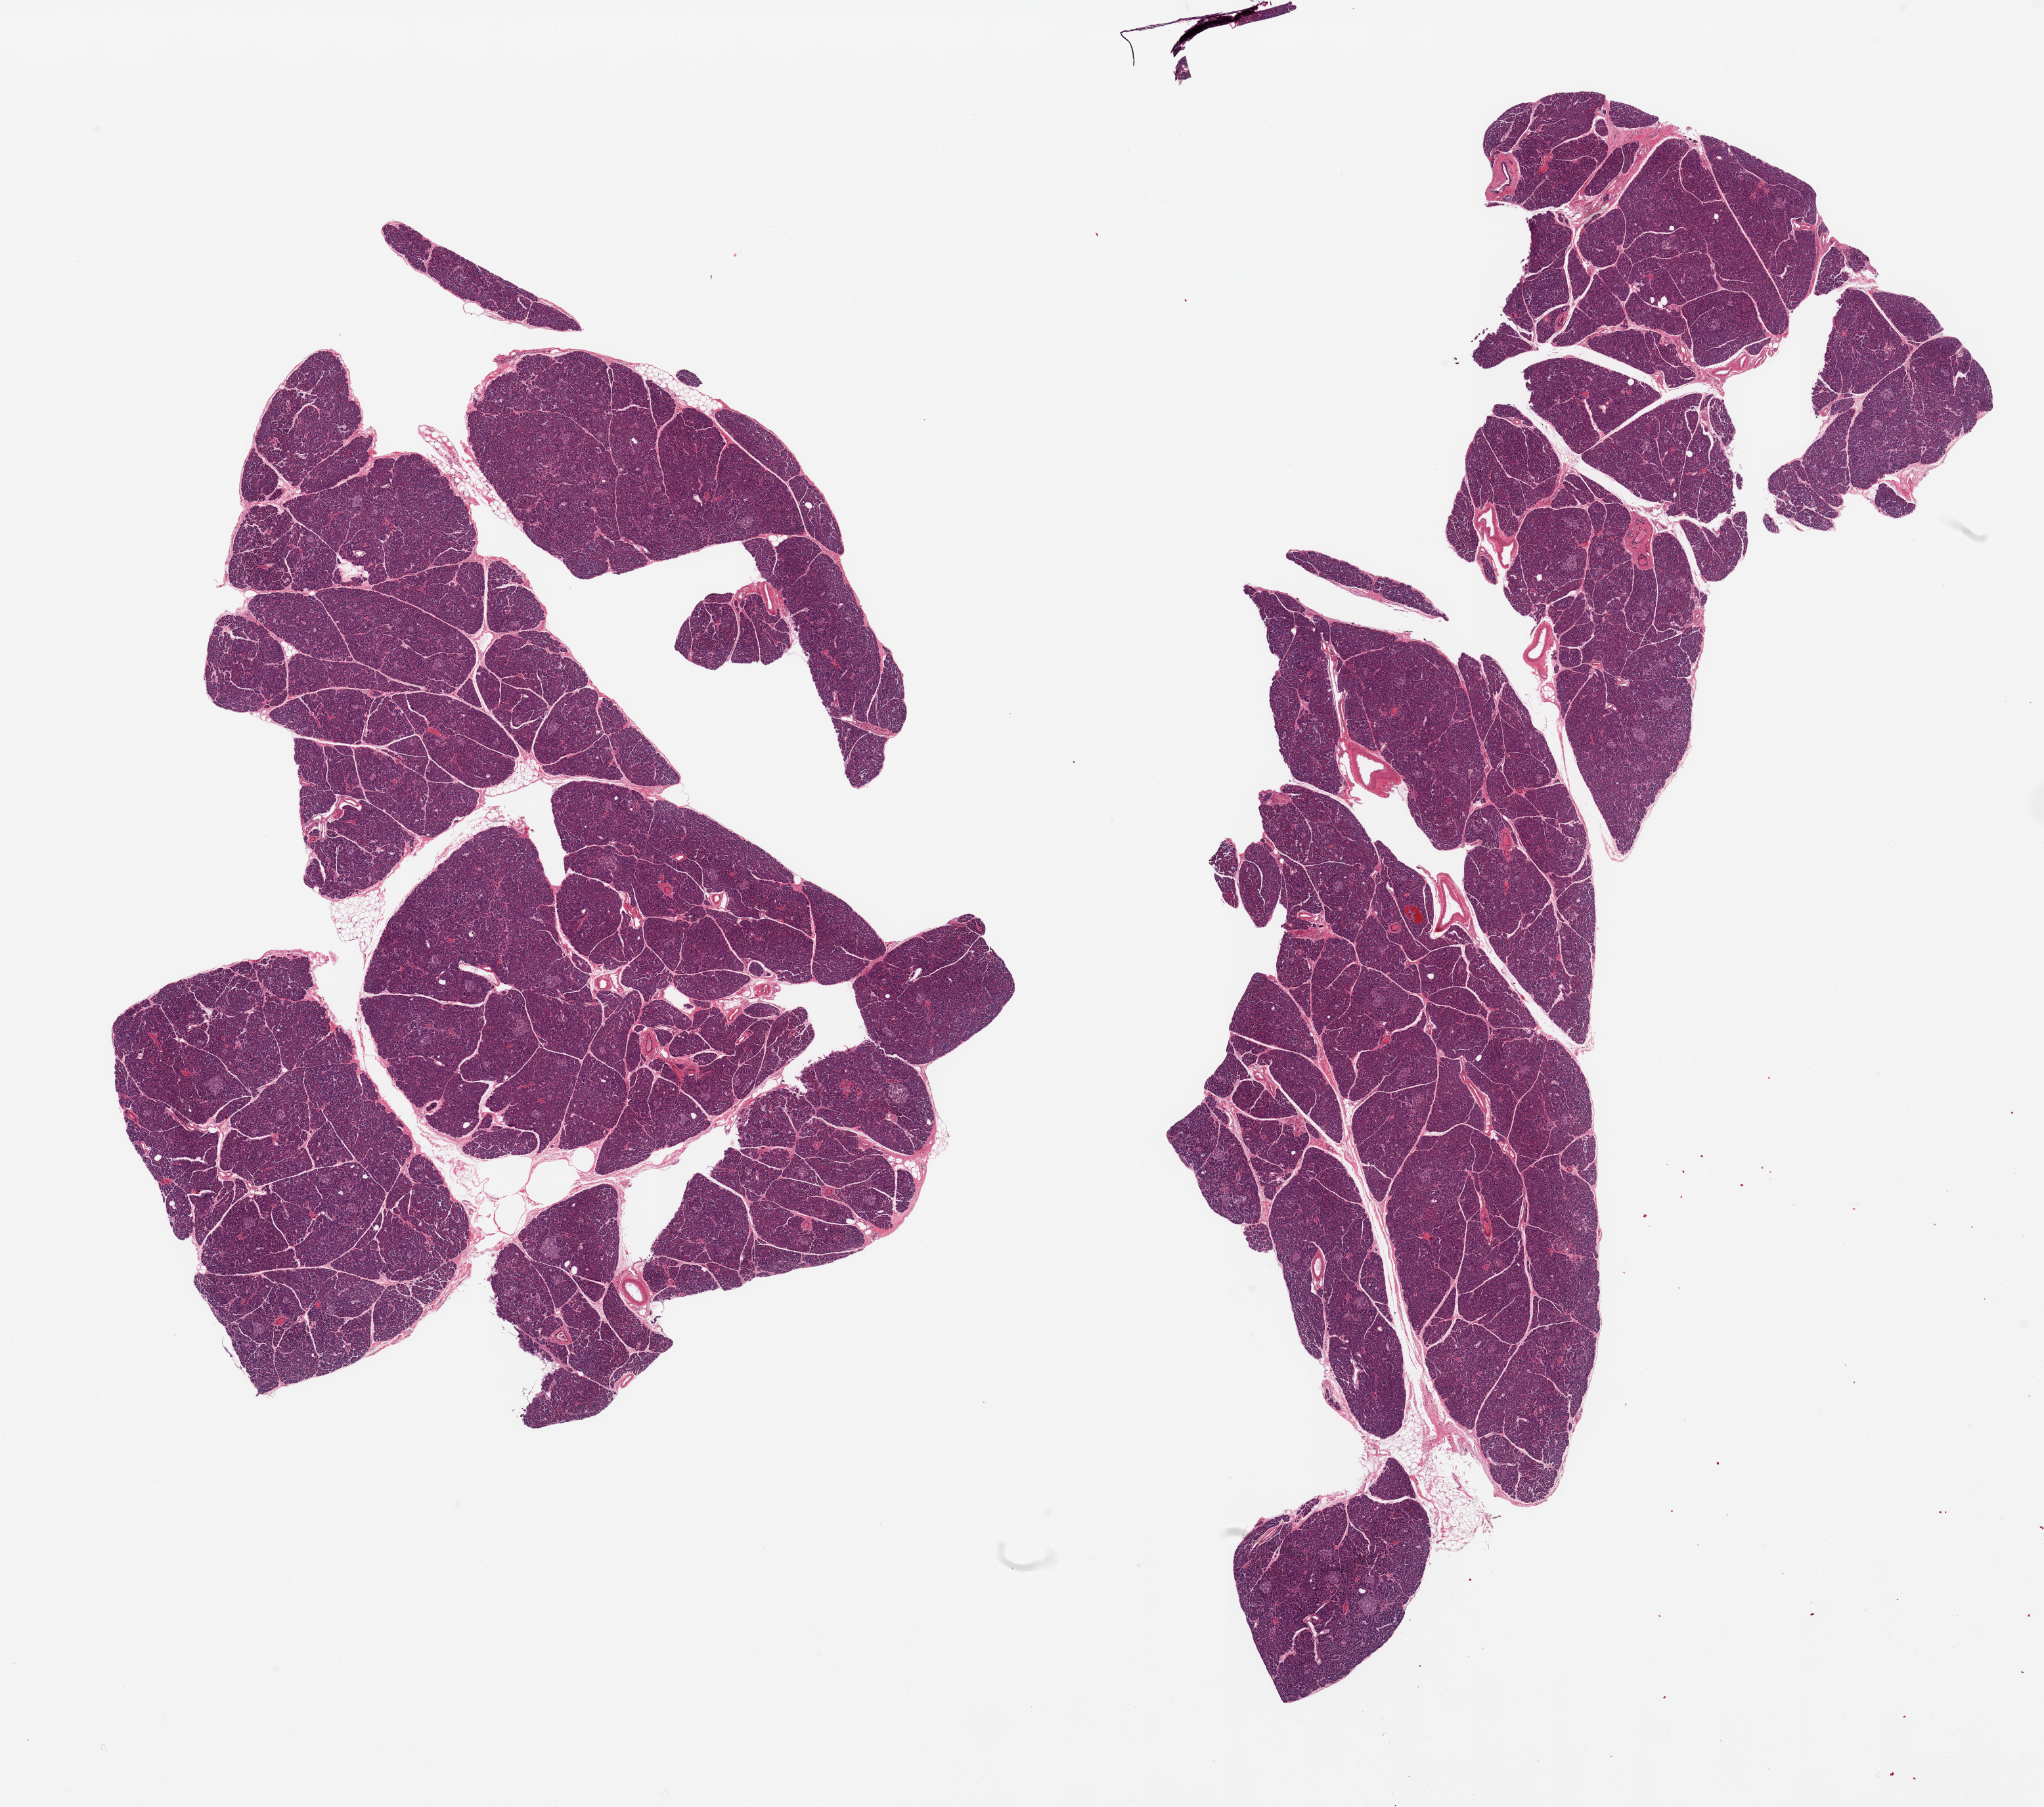
Digitized haematoxylin and eosin-stained section, whole scanned area (about 24.6 x 21.8 mm) shown as a low-resolution overview; PAXgene-fixed paraffin-embedded (PFPE) section; target tissue: pancreas; tissue donor sample. Male donor.
- reviewer comment on this tissue sample: 2 pieces, well preserved-- Islets well visualized, minimal fat